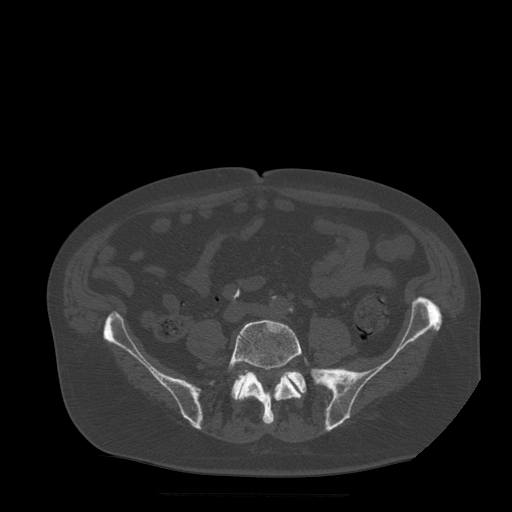
CT including the spine, one axial slice; bone window (W 1800 / L 400 HU); 512 × 512 image matrix. Patient age 72 years. Case-level facts recorded for this patient, not image findings: primary cancer: prostate.
Structures marked on this image (semi-automatically segmented with operator editing):
- L5 vertebra: bounding box <228,320,309,425> (left, top, right, bottom; pixels)